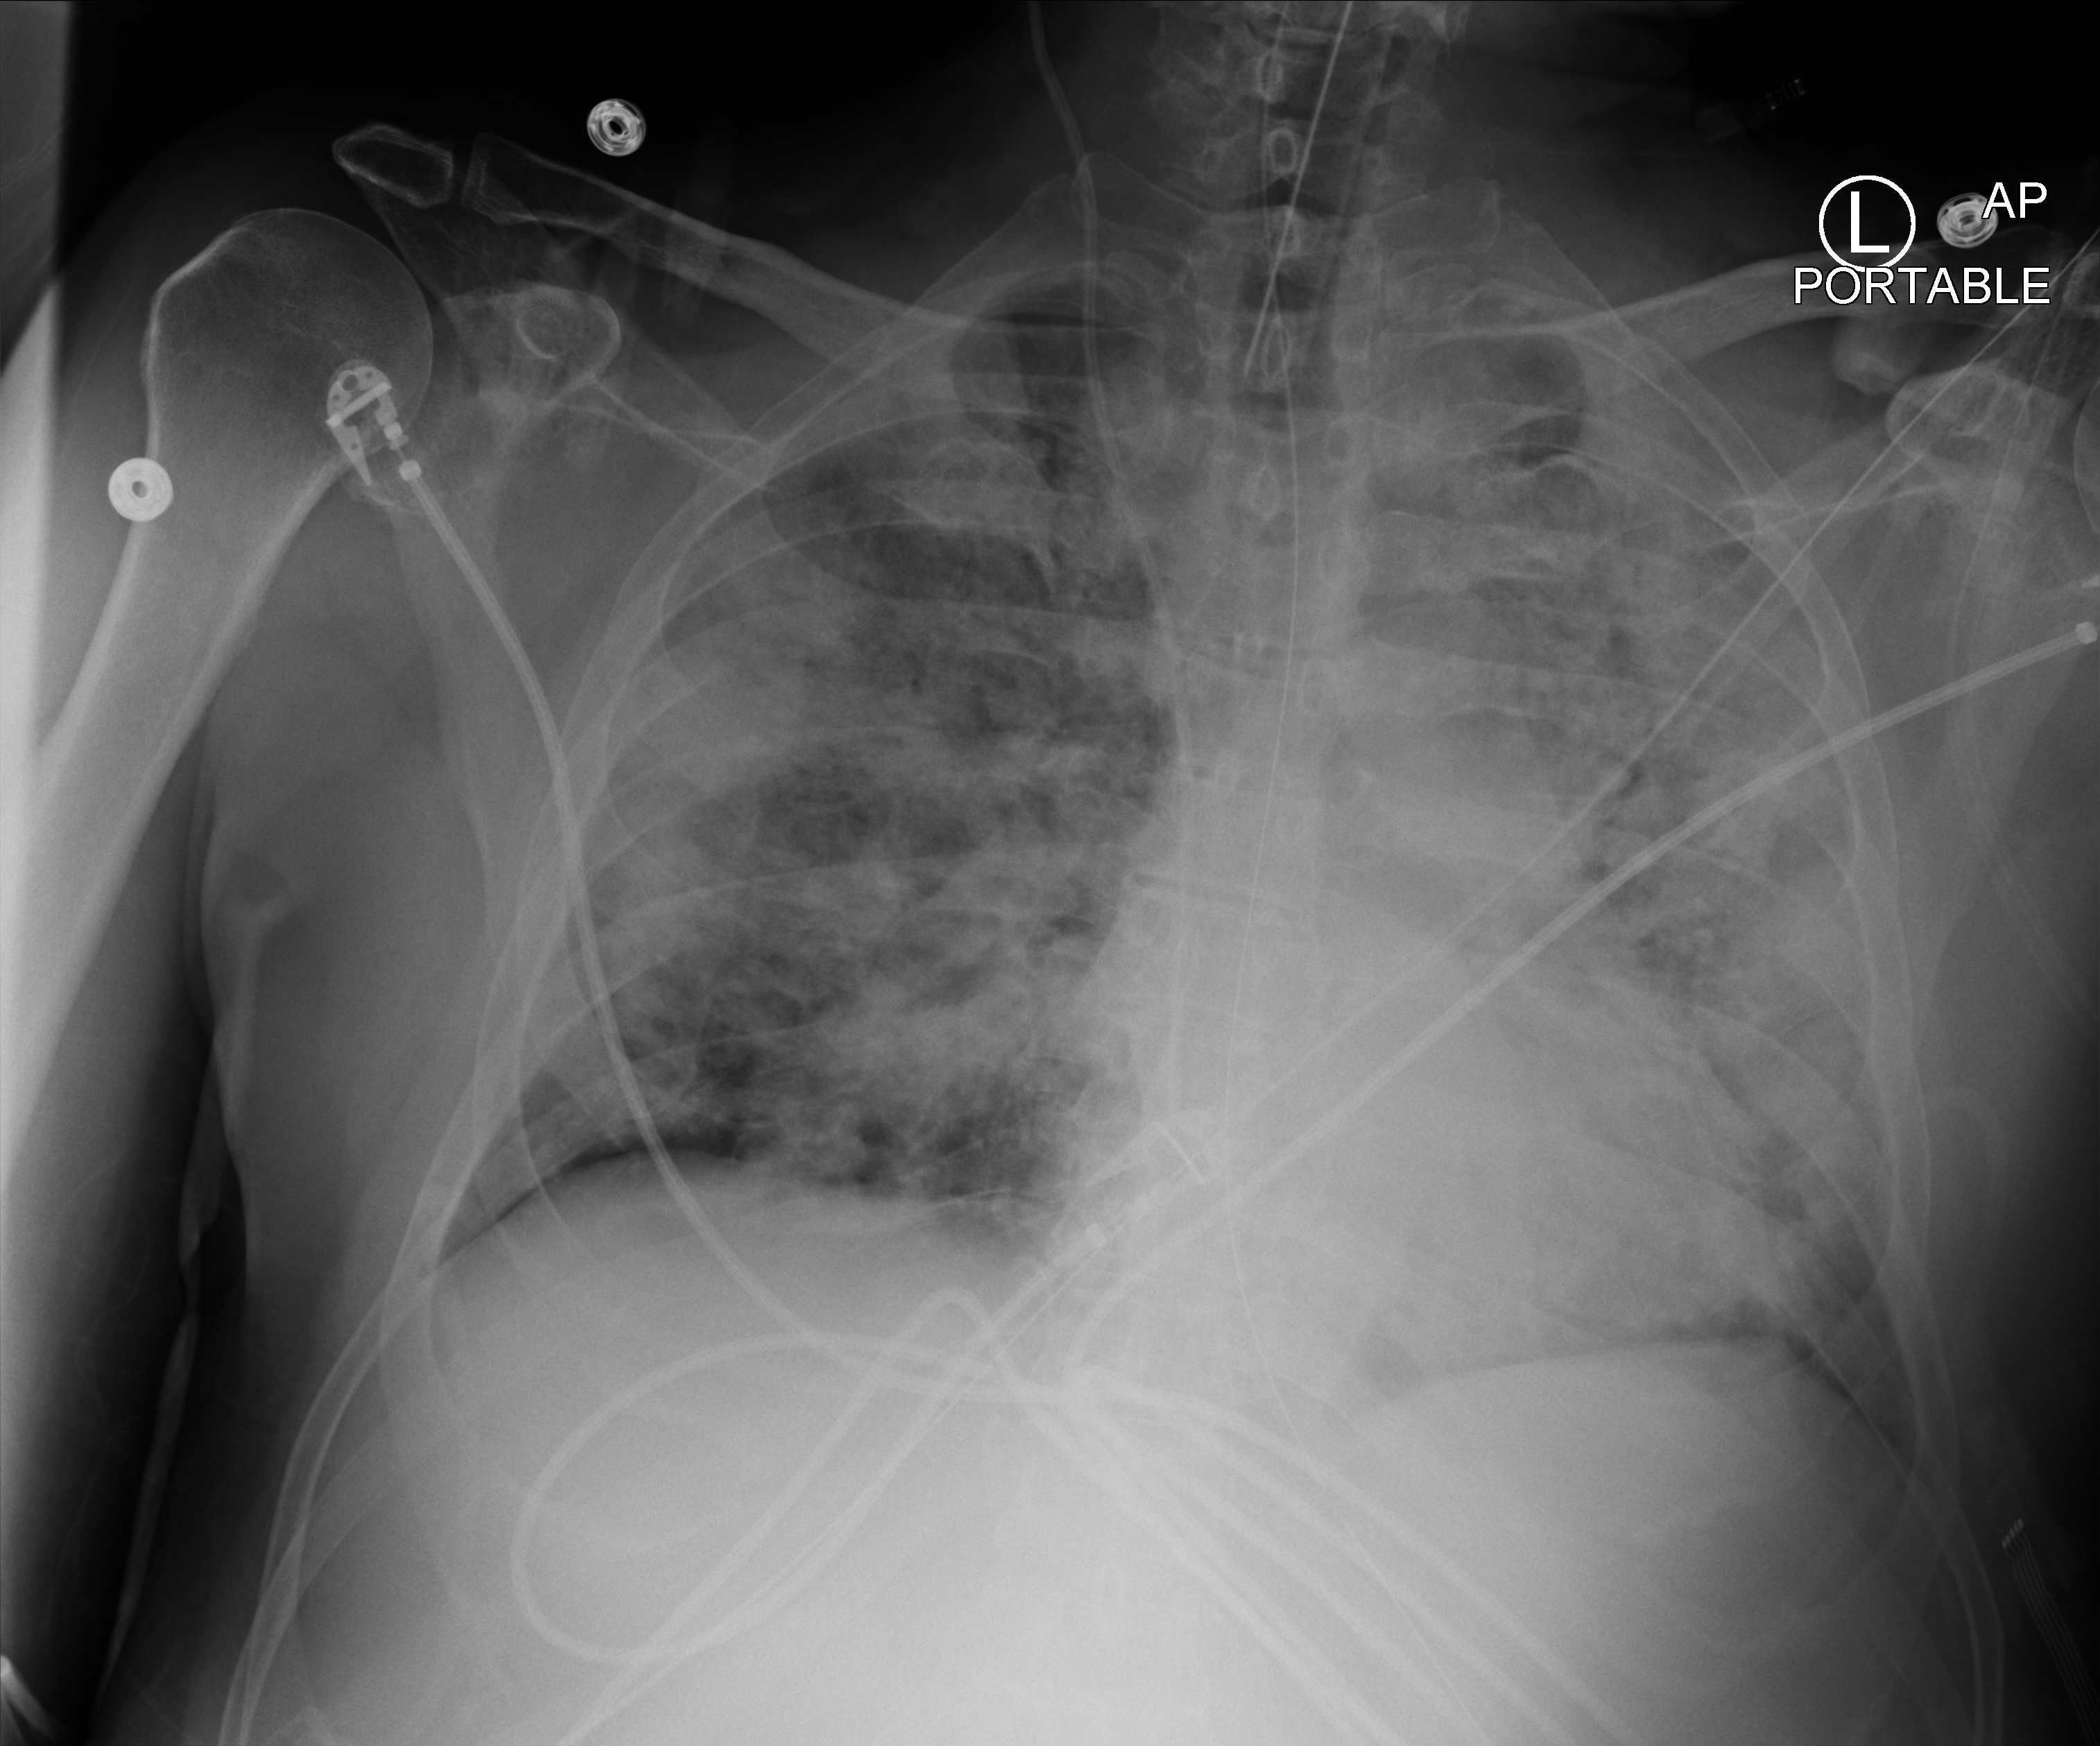
Bedside chest radiograph (computed radiography), anteroposterior (AP) projection. Patient hospitalised with COVID-19; male, aged 18–59 years.
Admission-level facts for this patient (not findings on this image; timing relative to this image not recorded):
- mechanically ventilated during this hospital stay: yes